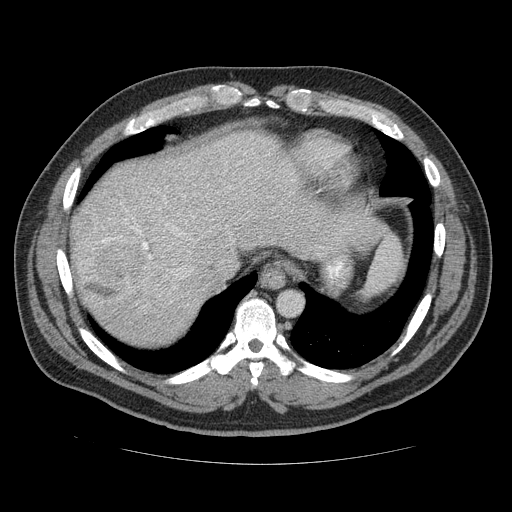
Contrast-enhanced abdominal CT (liver protocol), one axial slice. Position 101 of 113 along the scan axis. Reconstruction kernel STANDARD. 120 kVp. Soft-tissue window (W 400 / L 40 HU). 512 × 512 image matrix, field of view 400 × 400 mm. Case-level facts recorded for this patient, not image findings: diagnosis: hepatocellular carcinoma (patient treated with transarterial chemoembolisation; whether this scan precedes or follows treatment is not stated here); TNM stage (as recorded): Stage-II; Child-Pugh class: B.
Annotated regions visible in this slice (semi-automatic segmentation, software-assisted and operator-edited):
- abdominal aorta: bounding box [x1, y1, x2, y2] px = [279, 292, 301, 315]
- liver parenchyma outside the tumour (the mass and vessels are separate outlines, so this box may not span the whole liver): [70, 134, 386, 340]
- mass: [72, 211, 174, 299]
- liver vessels: [96, 220, 153, 261]